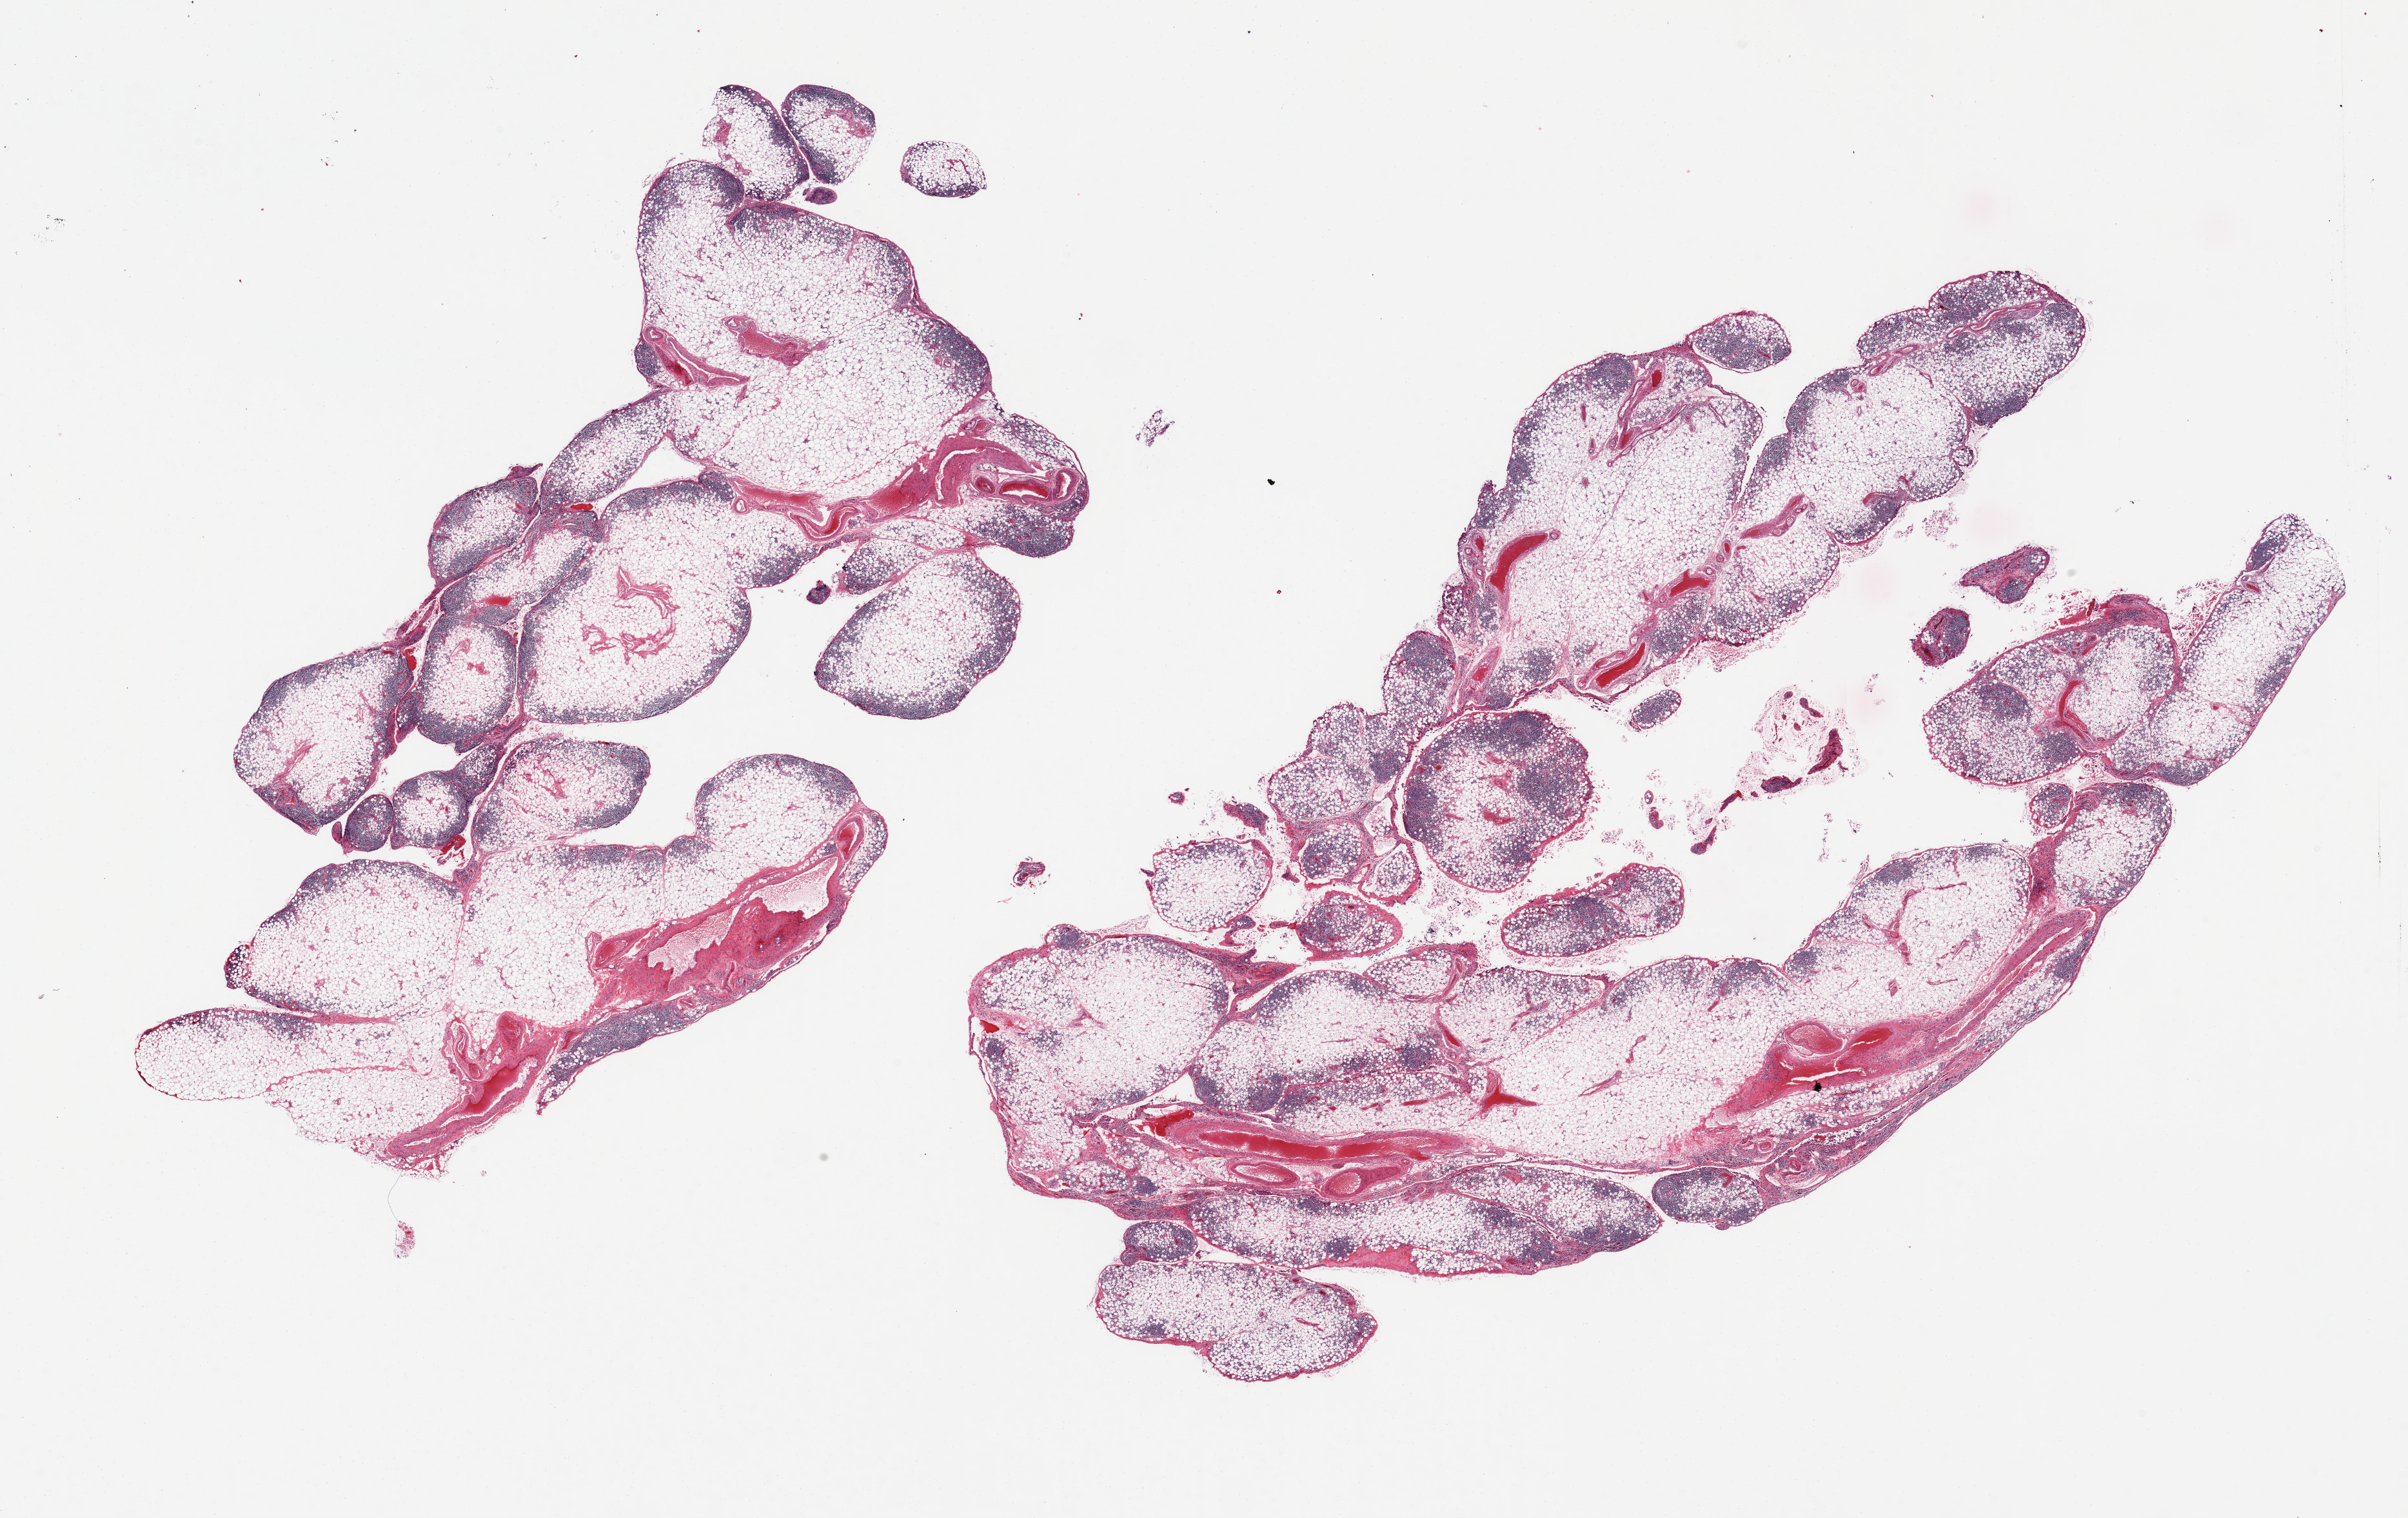
Whole-slide image, hematoxylin and eosin (H&E) stain, brightfield — shown as a low-resolution overview of the whole scanned area (about 29.5 x 18.6 mm, slide scanned at 20x). PAXgene-fixed, paraffin-embedded tissue. Target tissue: omentum. Donor tissue sample.
* review note (as recorded): 2 pieces, diffuse chronic inflammation/mesenteritis; rep lymphoid aggregates